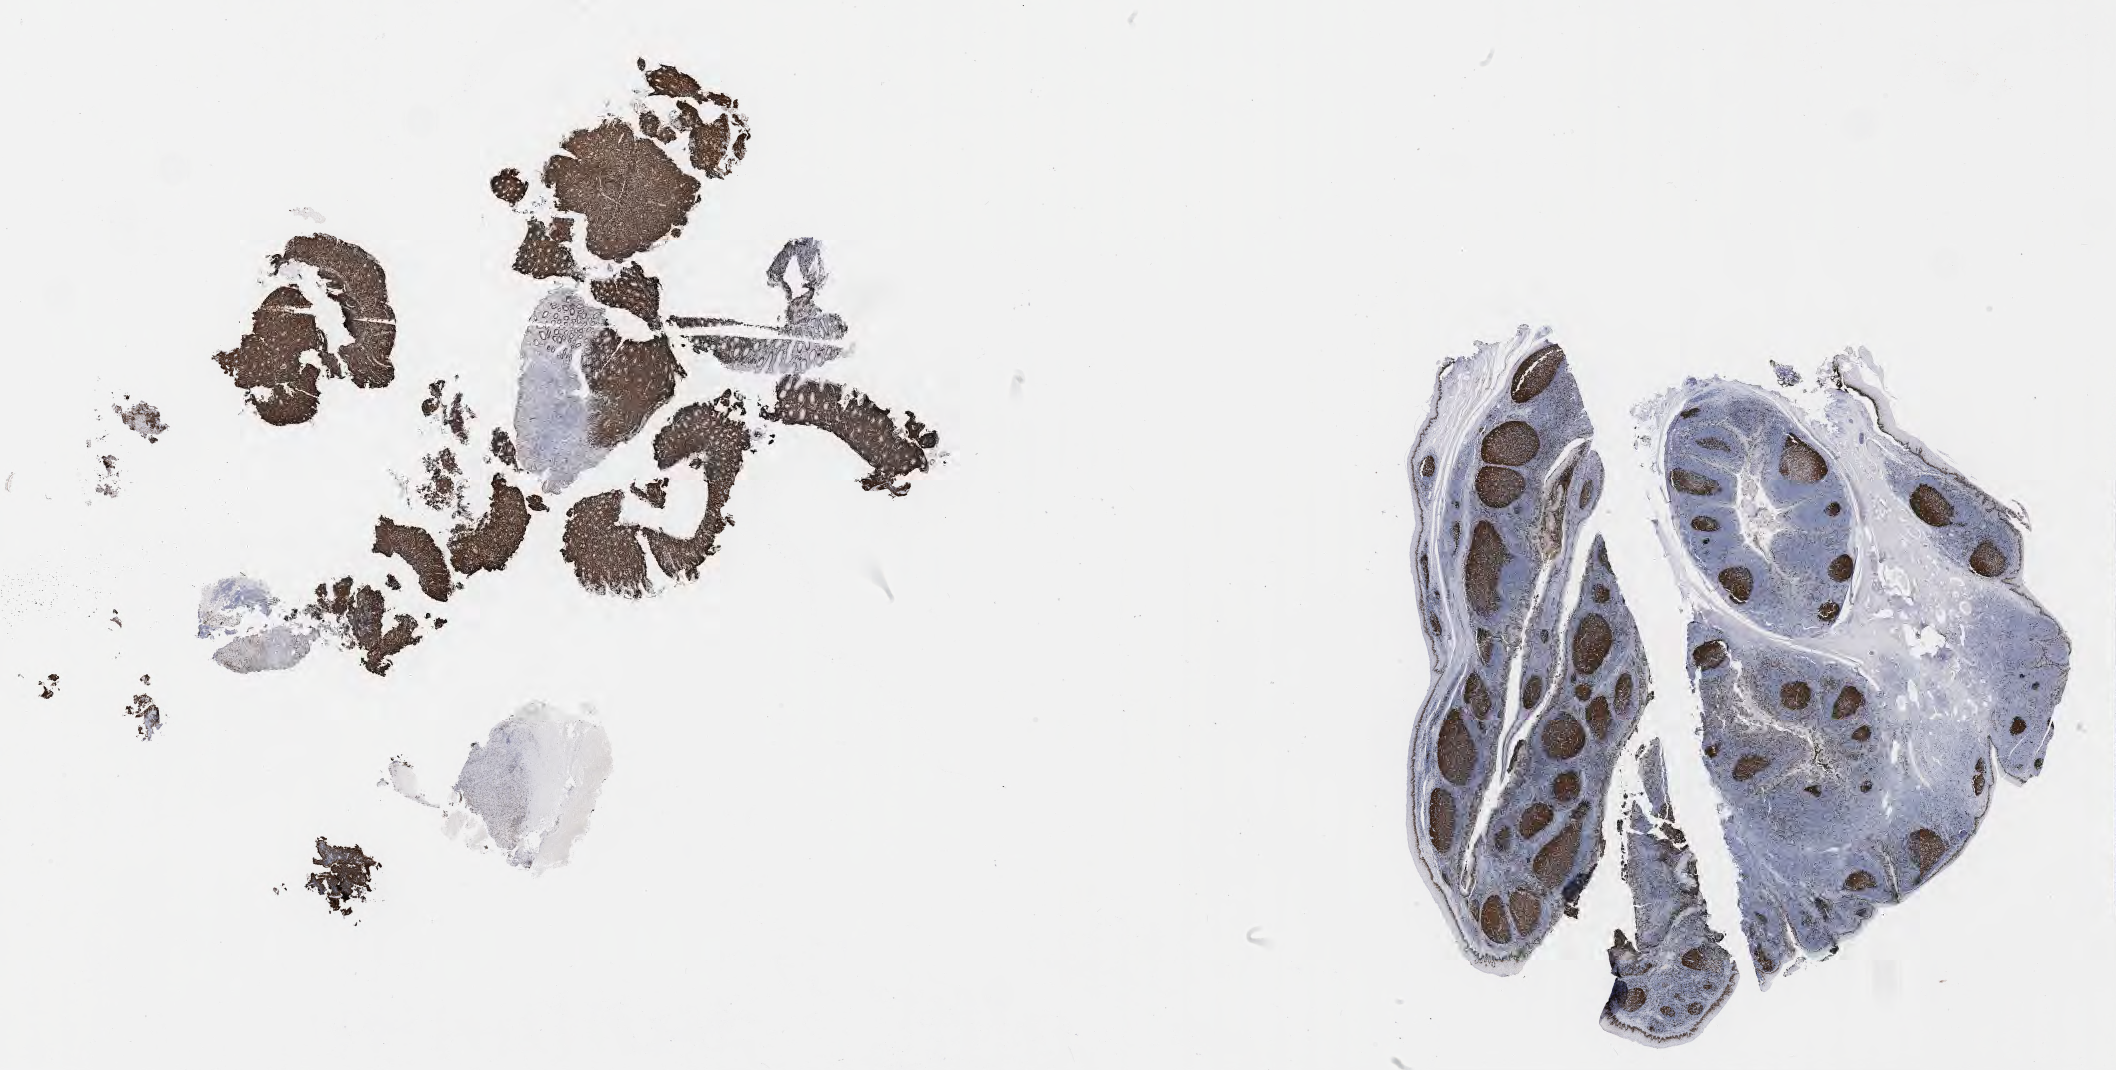
Whole-slide image, immunohistochemical stain for Ki-67, low-resolution overview of the scanned area, about 34.2 x 17.3 mm; tumor tissue. Male patient, aged 56.
* histologic diagnosis: Burkitt lymphoma, NOS